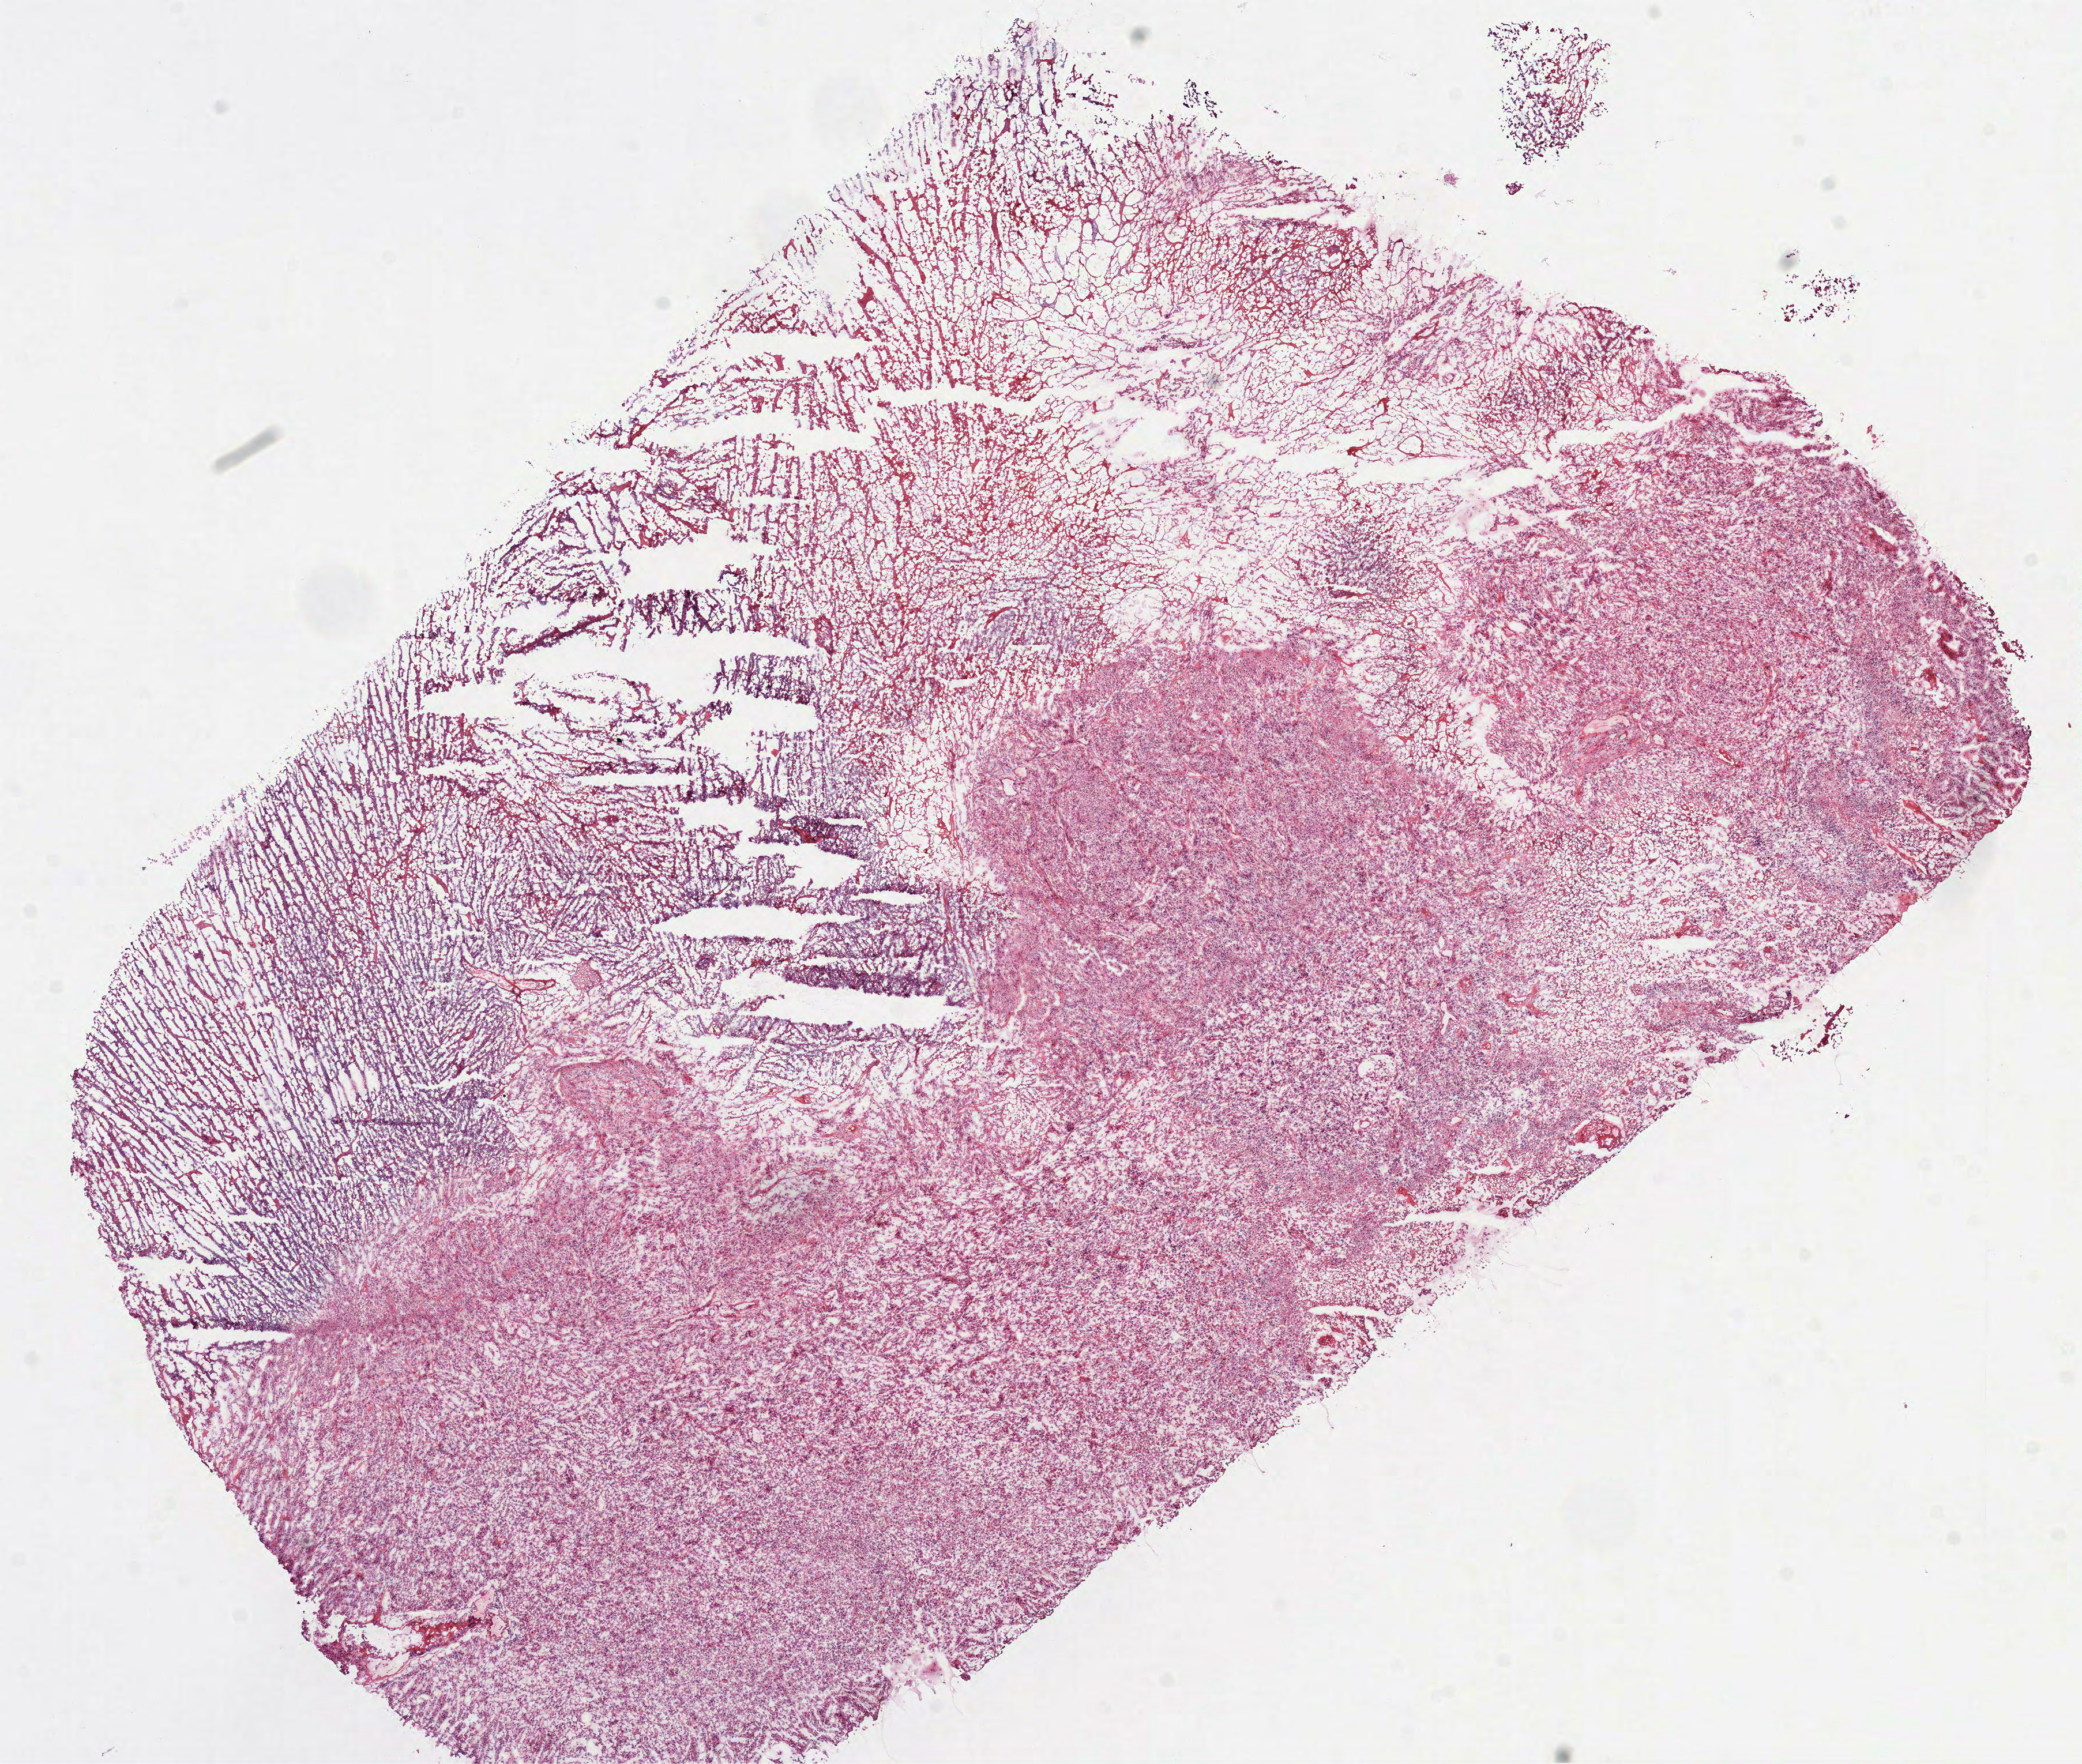
Digitized Hematoxylin and eosin (H&E) stained tissue section (whole slide) — low-resolution overview of the scanned area, about 14.6 x 12.3 mm (slide scanned at 40x); frozen section from the top of the tissue portion; primary tumour sample from the brain. Male patient; age at initial diagnosis 58 years. Composition of this section per pathologist review: tumour cells 60%, tumour nuclei 80%, normal cells 0%, stromal cells 0%, necrosis 40%.
* pathologic diagnosis: Glioblastoma